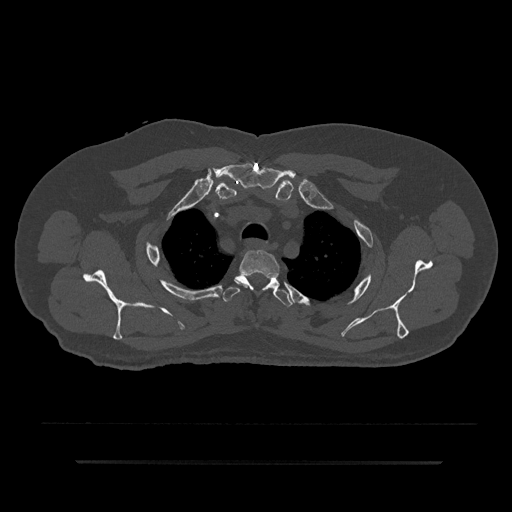
CT including the spine, one axial slice. Position 678 of 797 along the scan axis. Reconstruction kernel Br40s/3. Bone window (W 1800 / L 400 HU). 0.5 mm slice thickness. 512 × 512 image matrix. Patient: male, 59 years. Case-level facts recorded for this patient, not image findings: primary cancer: bile ducts; vertebrae with lytic lesions (as recorded): T10.
Structures marked on this image (semi-automatically segmented with operator editing):
- T2 vertebra: box from (x=235, y=250) to (x=280, y=293) px
- T3 vertebra: (x=223, y=275)–(x=293, y=307)